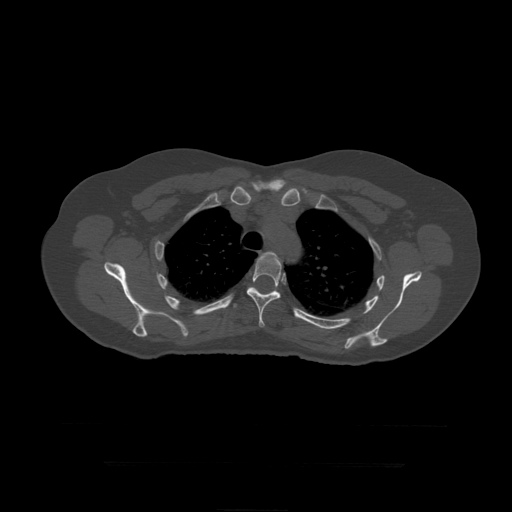
CT including the spine, one axial slice; slice 335 of 399 in the series (ordered by position); bone window (W 1800 / L 400 HU); 1.25 mm slice thickness; 512 × 512 image matrix. Patient age 41 years. From the clinical record (not read from this slice): primary cancer: breast.
Annotated regions visible in this slice (semi-automatic segmentation, software-assisted and operator-edited):
- T4 vertebra: bounding box <255,252,282,270> (left, top, right, bottom; pixels)
- T5 vertebra: <247,252,282,328>
- T6 vertebra: <234,291,274,308>